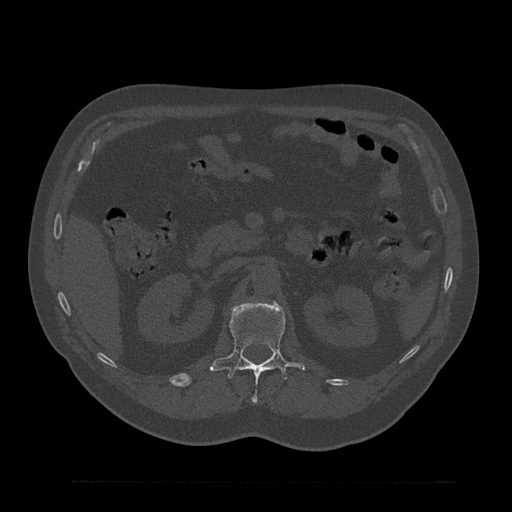
CT including the spine, one axial slice. Slice 165 of 797 in the series (ordered by position). 120 kVp. Bone window (W 1800 / L 400 HU). 0.5 mm slice thickness. 512 × 512 image matrix. Patient: male, 61 years. Case-level facts recorded for this patient, not image findings: primary cancer: prostate.
Annotated regions visible in this slice (semi-automatic segmentation, software-assisted and operator-edited):
- L1 vertebra: bounding box [x1, y1, x2, y2] px = [210, 301, 305, 402]